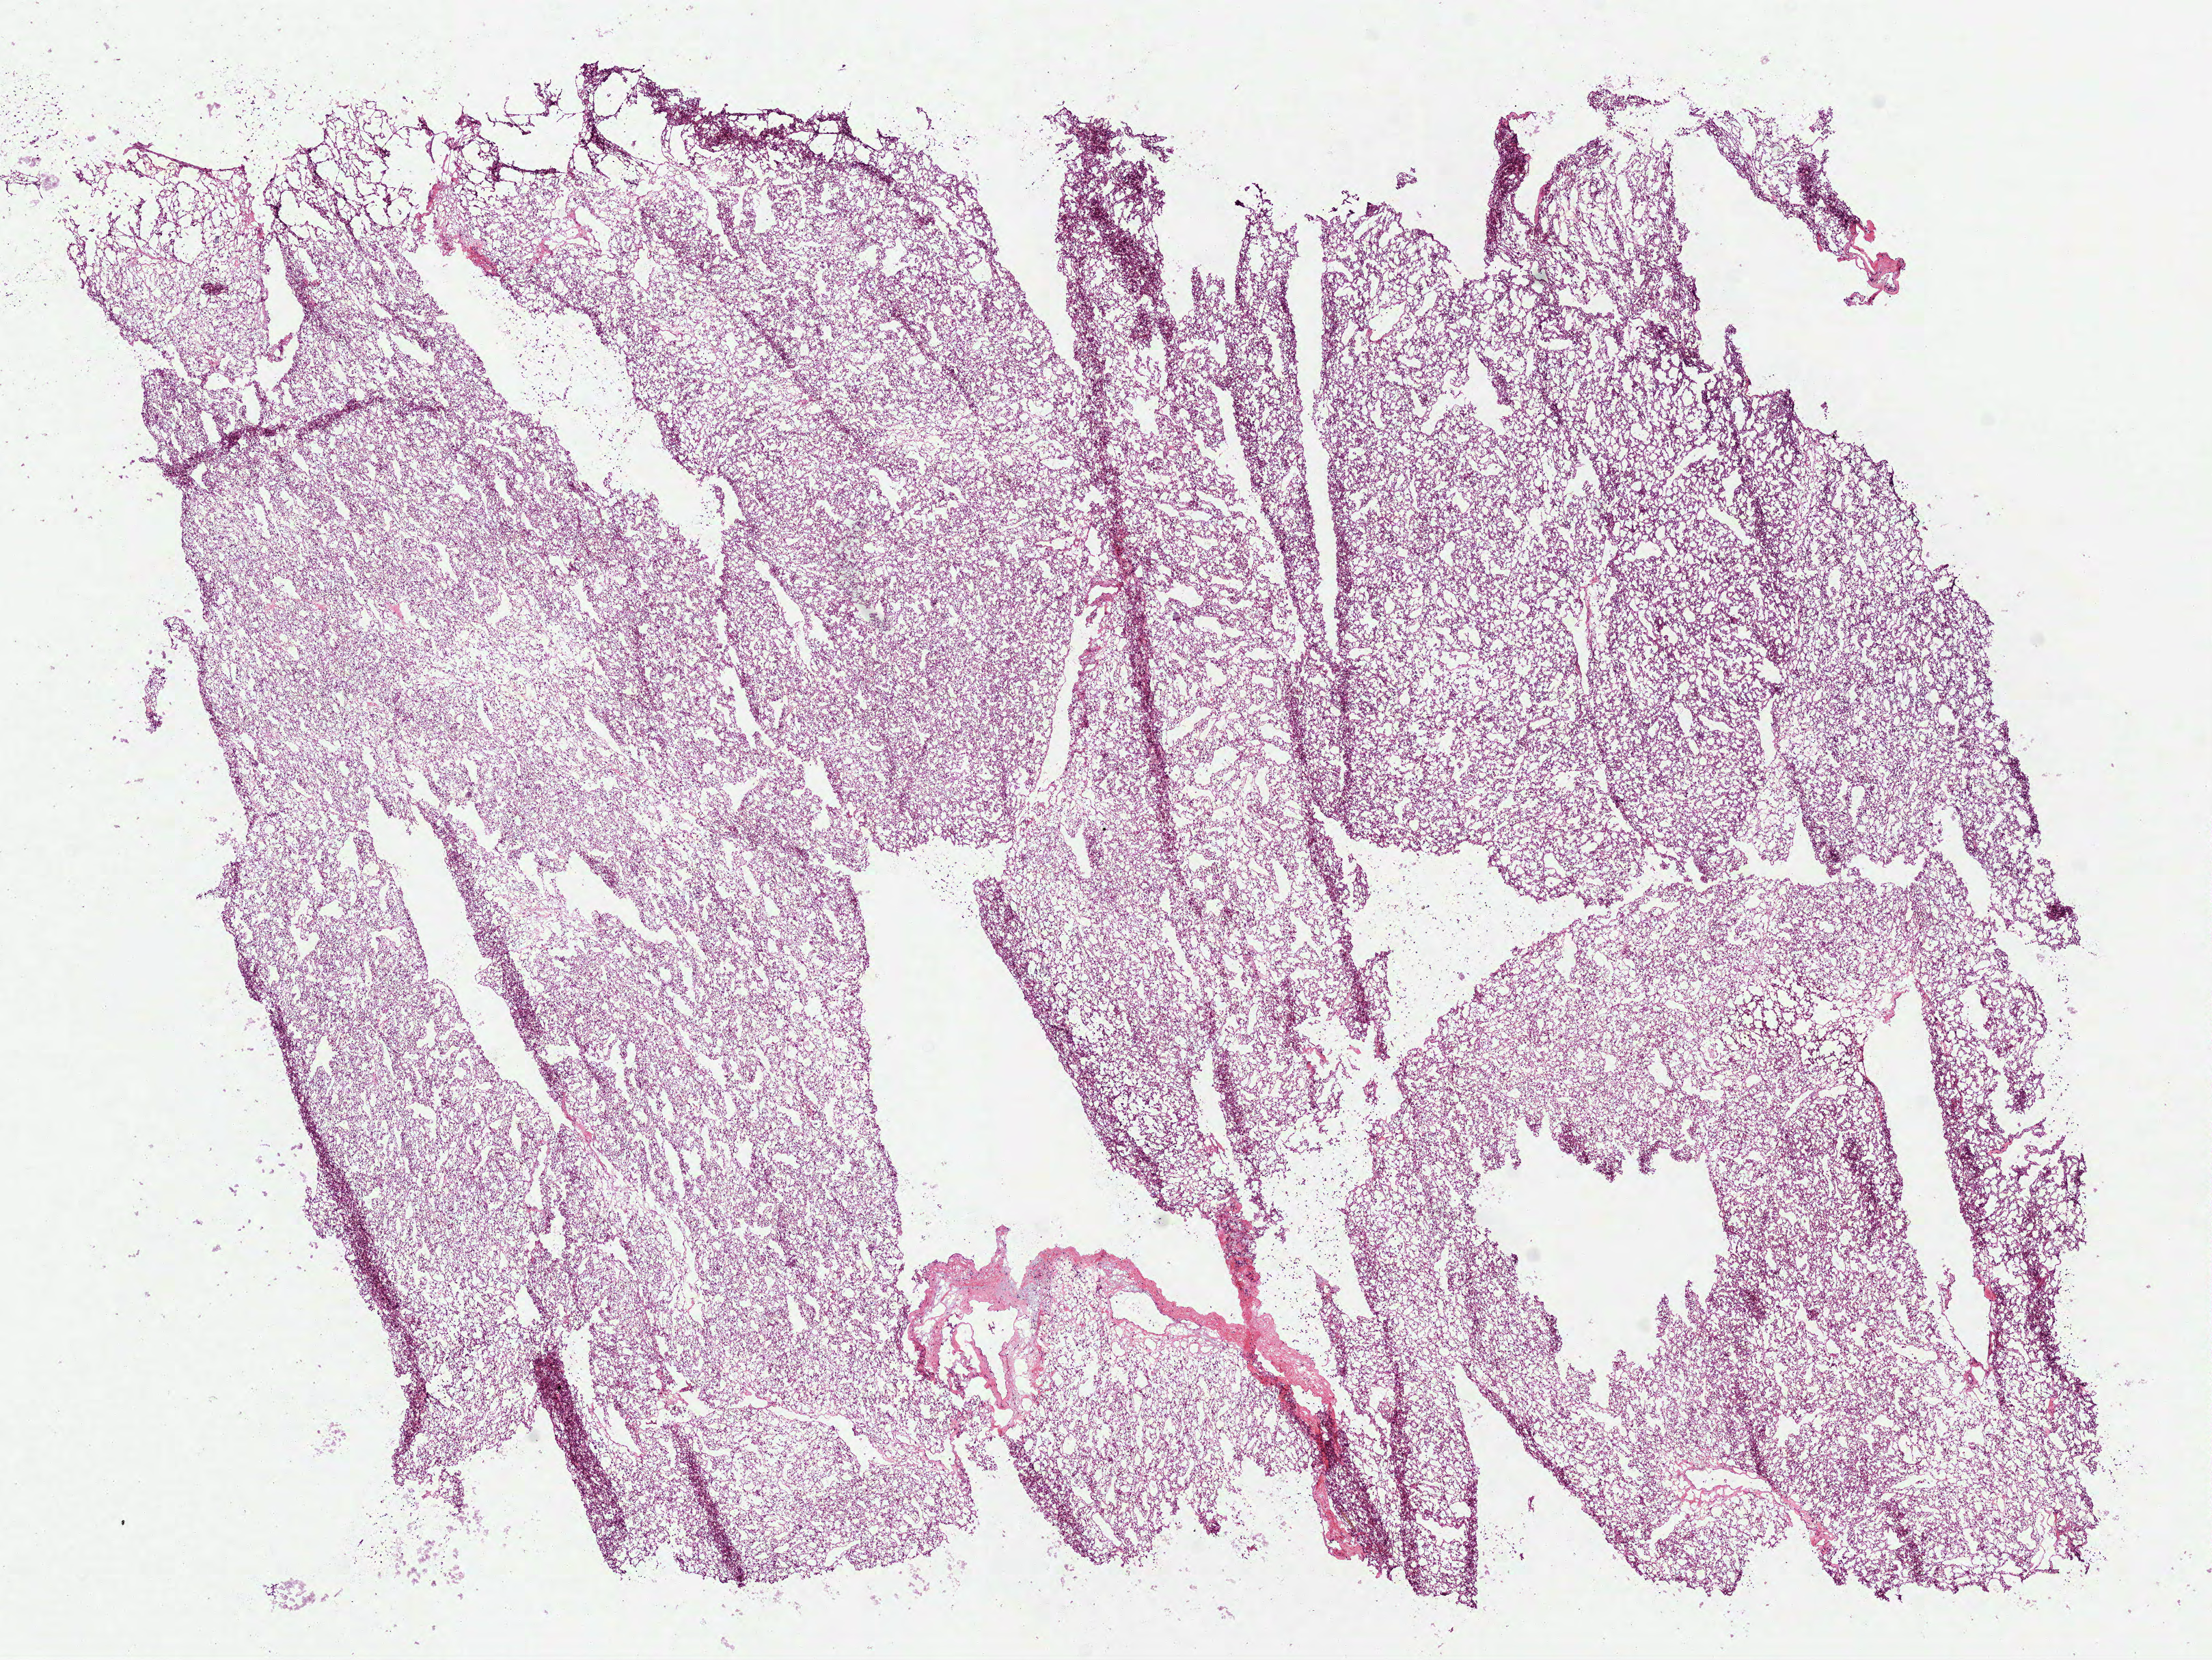
H&E whole-slide image — low-resolution overview of the scanned area, about 13.1 x 9.8 mm (acquisition: 40x scan); frozen section; sample: primary tumour, kidney. Female, age 63 years at initial diagnosis. Histologic grade: G3 (poorly differentiated). Pathologist review of this section (percent, as recorded): tumour cells 90%, tumour nuclei 80%, normal cells 0%, stromal cells 10%, necrosis 0%.
Laterality: right. Histologic diagnosis: Clear cell adenocarcinoma, NOS. AJCC pathologic stage: II (6th edition).